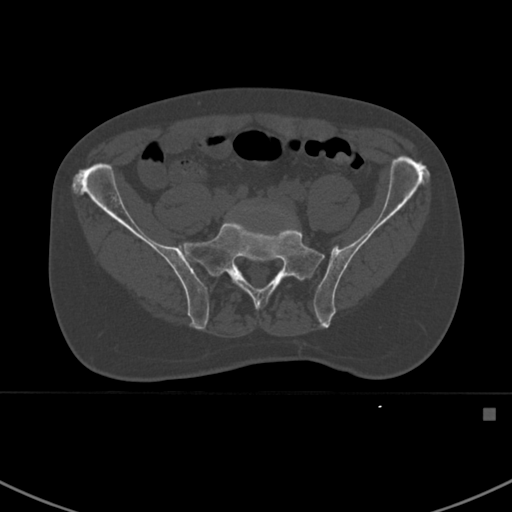
CT including the spine, one axial slice. Bone window (W 1800 / L 400 HU). 1.5 mm slice thickness. 512 × 512 image matrix. Male patient, age 59 years. Case-level facts recorded for this patient, not image findings: primary cancer: prostate.
Structures marked on this image (semi-automatic segmentation, software-assisted and operator-edited):
- L5 vertebra: bounding box <242,206,287,218> (left, top, right, bottom; pixels)